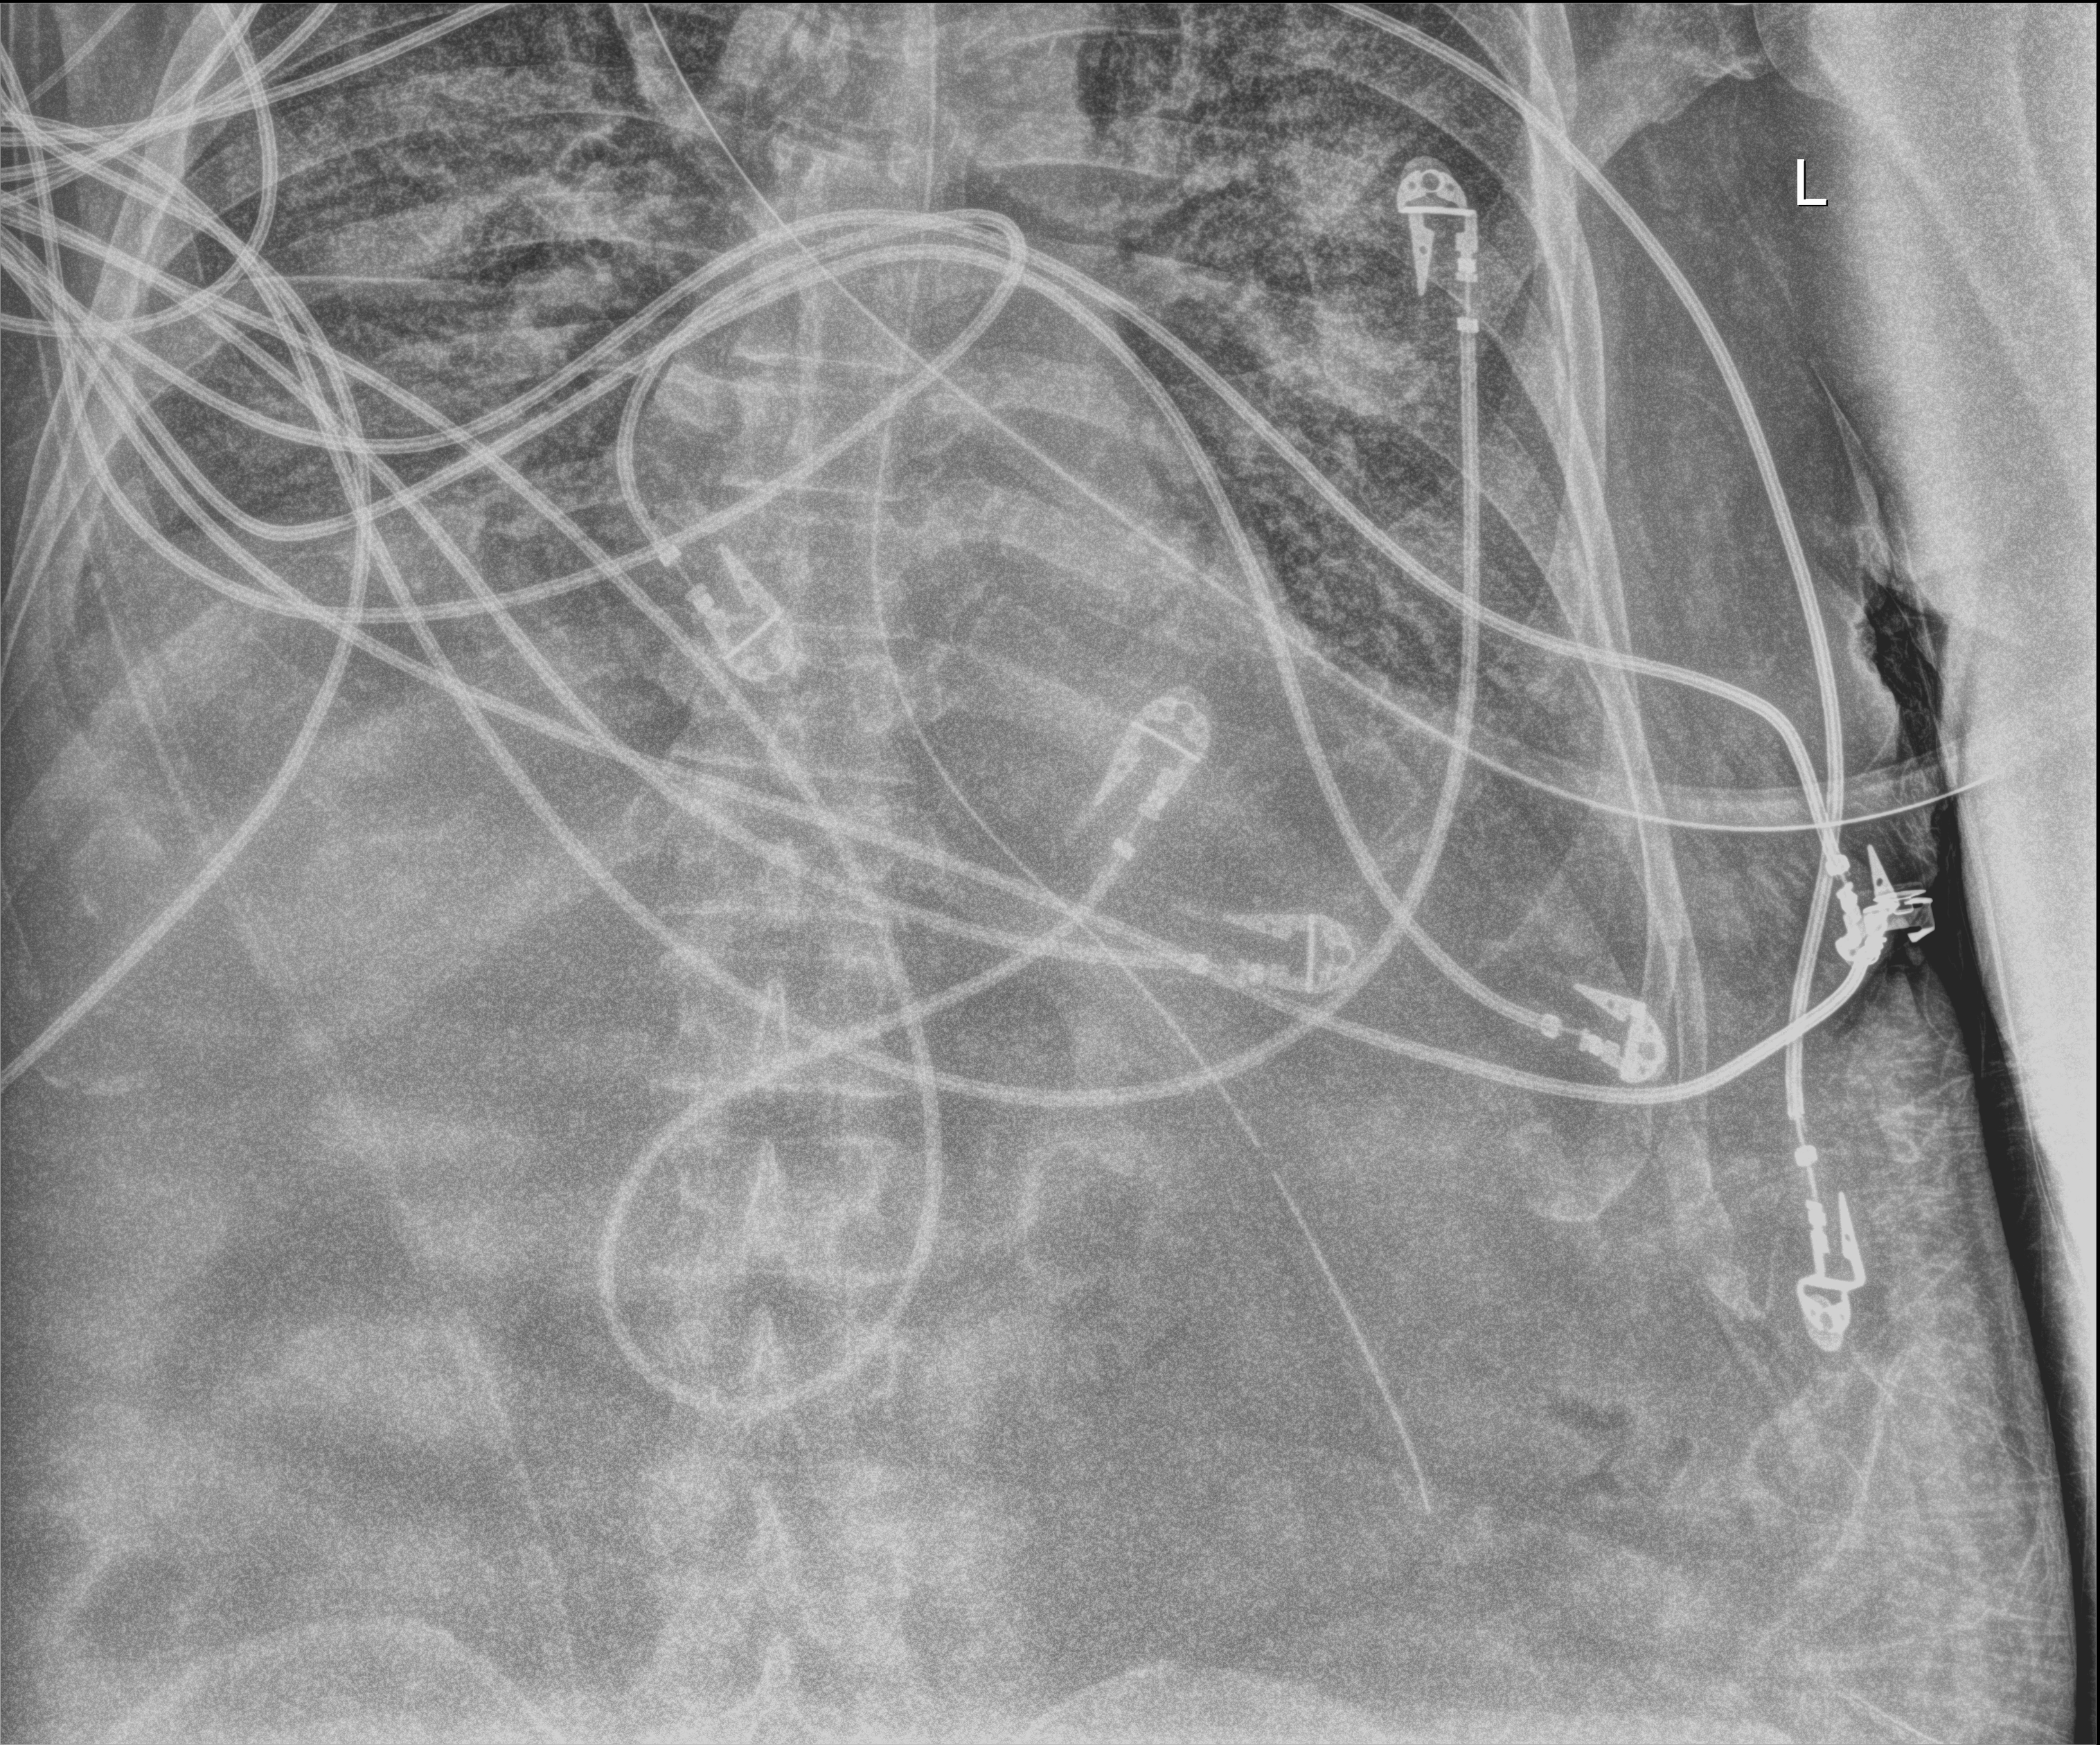
Chest X-ray (portable), anteroposterior (AP) projection. Patient hospitalised with COVID-19; male, aged 60–74 years.
Admission-level facts for this patient (not findings on this image; timing relative to this image not recorded): length of hospital stay: 24 days.